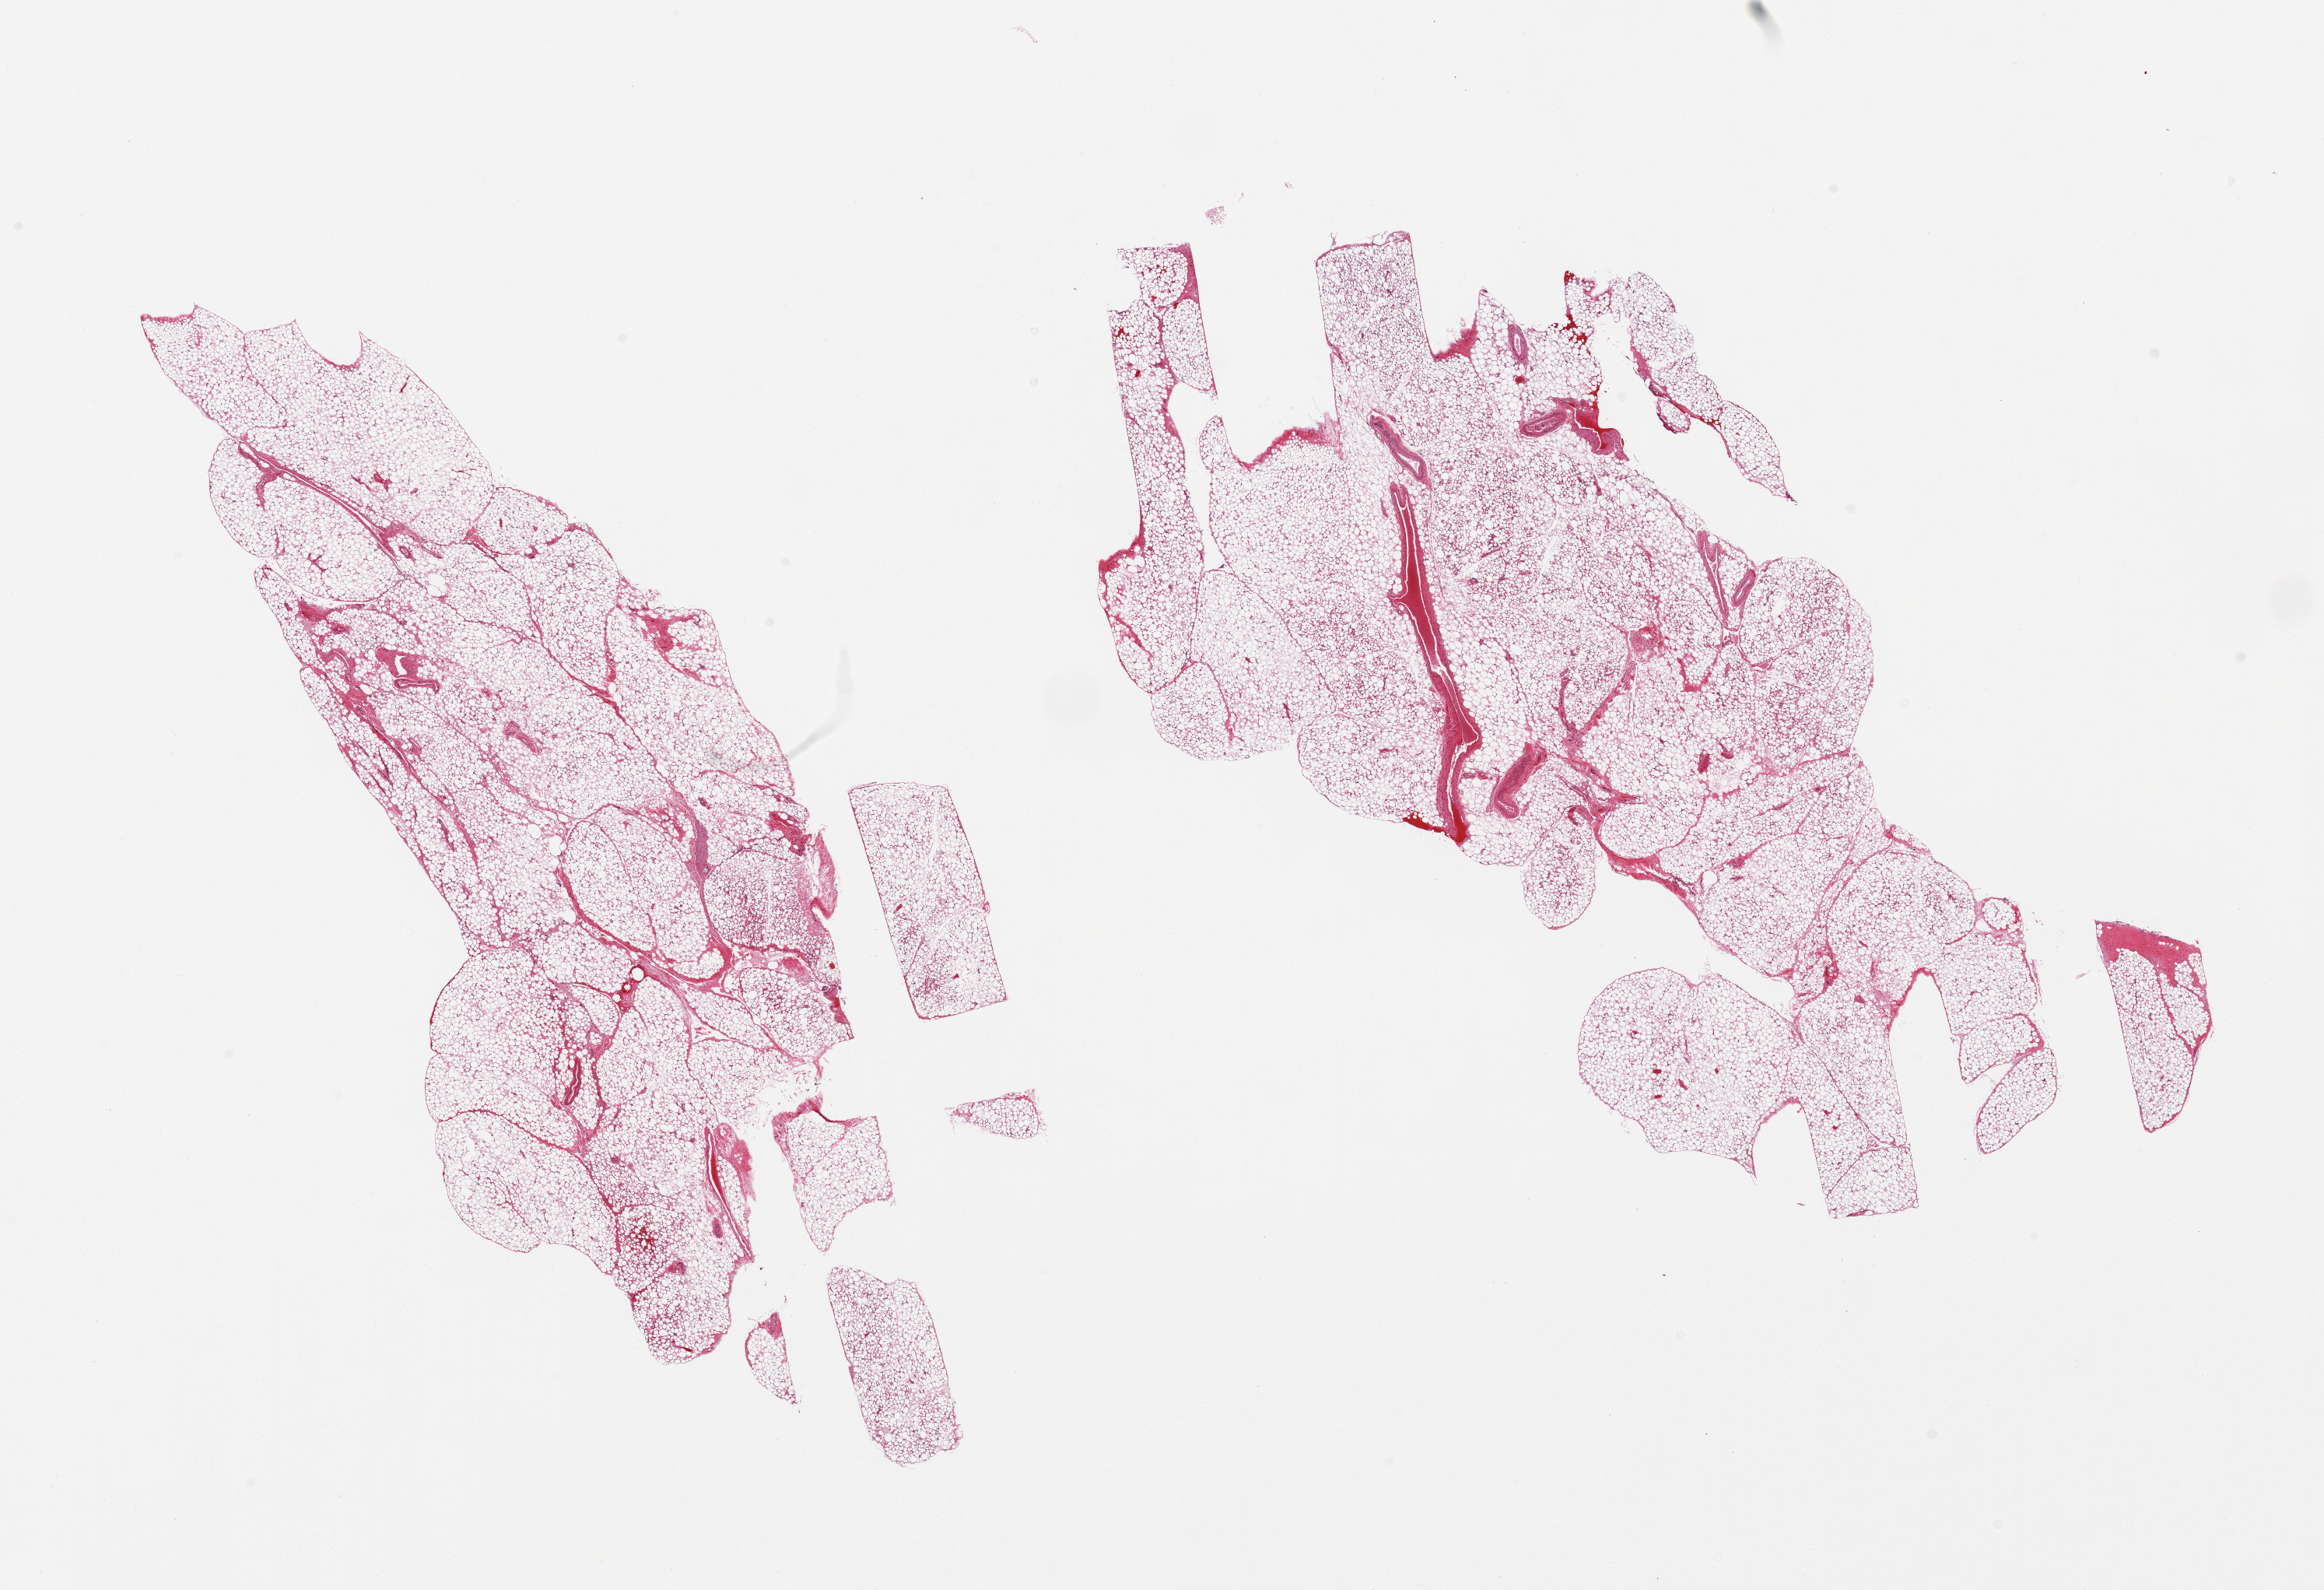
Digitized hematoxylin and eosin (H&E)-stained section — a low-resolution overview of the entire scanned area, about 23.6 x 16.2 mm (from a 20x scan), PAXgene-fixed, paraffin-embedded tissue, target tissue: omentum, donor tissue sample. Donor sex: female.
Reviewer comment on this tissue sample: 2 pieces; fat with about 5% fibrovascular tissue.